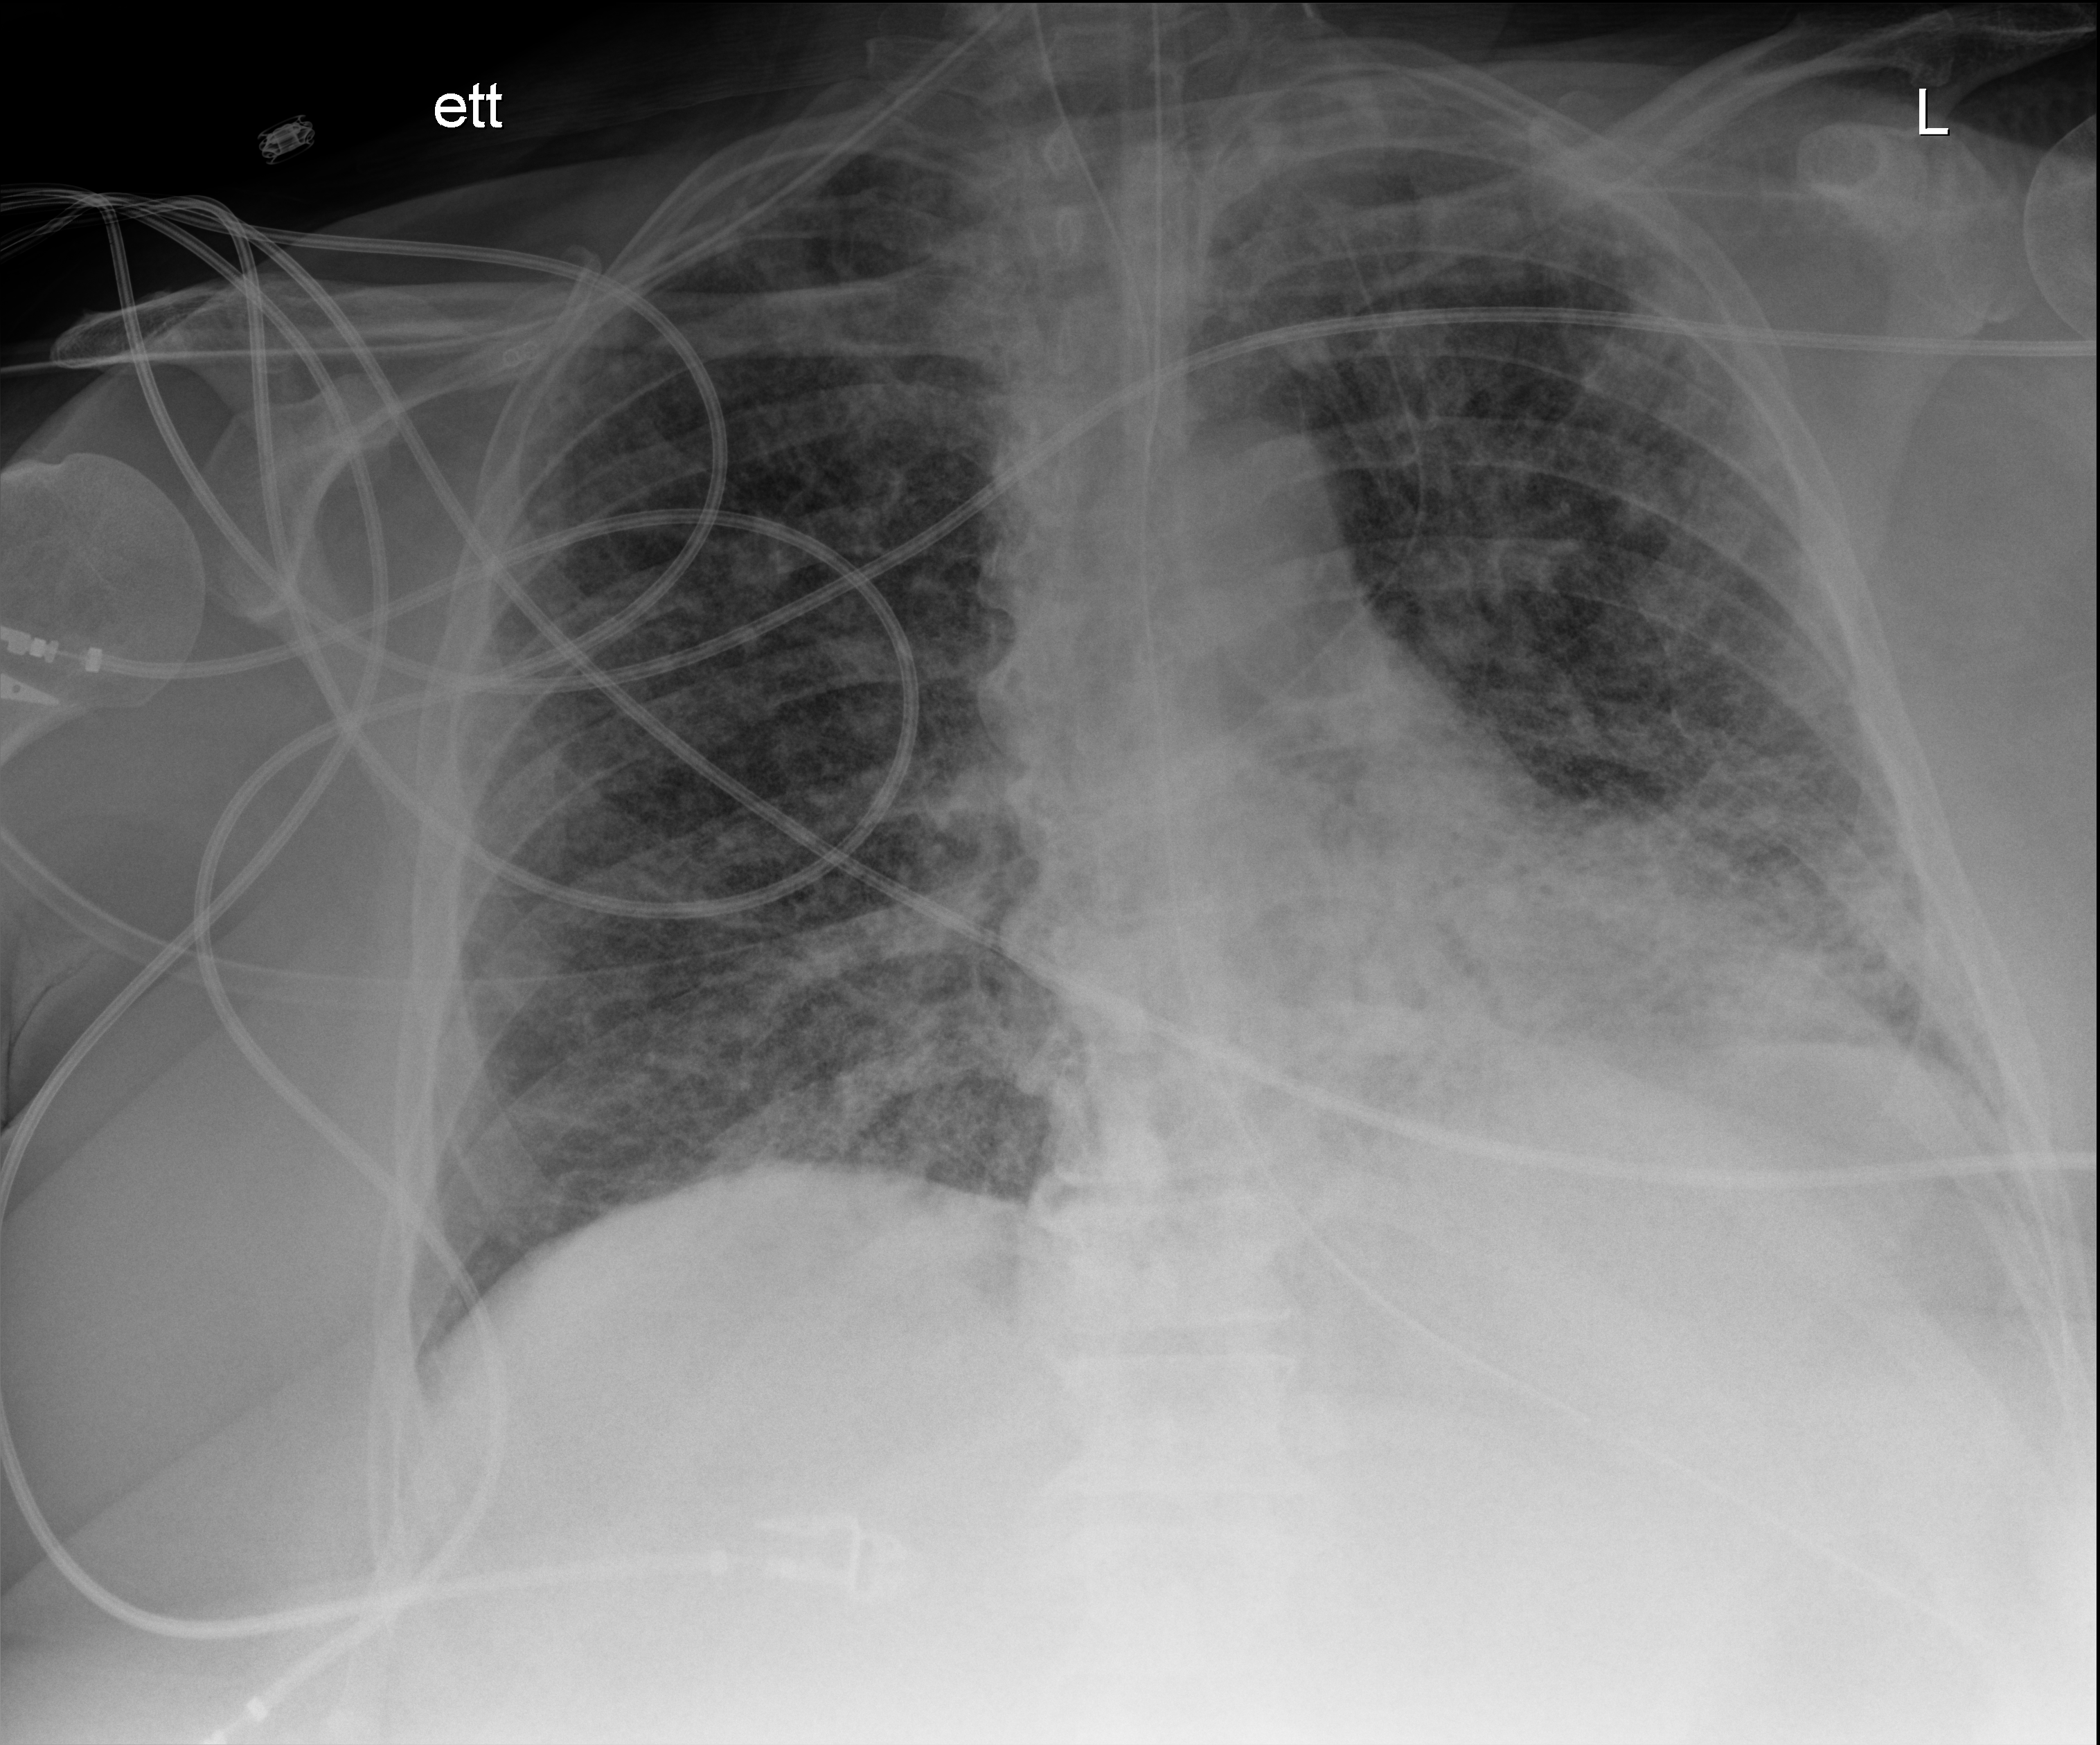
Portable chest radiograph. Adult patient hospitalised with COVID-19, age 18–59 years.
Hospital-stay facts (about this admission, not read from this image; timing relative to this image not recorded):
- admitted to intensive care during this hospital stay: yes
- mechanically ventilated during this hospital stay: yes
- length of hospital stay: 28 days